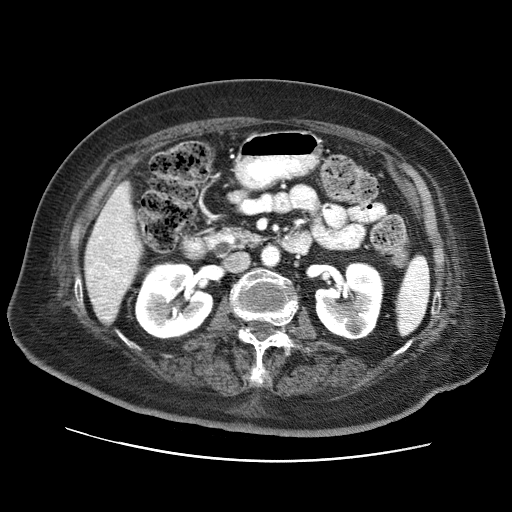
Contrast-enhanced abdominal CT (liver protocol), one axial slice; position 24 of 73 along the scan axis; 120 kVp; soft-tissue window (W 400 / L 40 HU); 2.5 mm slice thickness; 512 × 512 image matrix, field of view 380 × 380 mm. From the clinical record (not read from this slice): diagnosis: hepatocellular carcinoma (patient treated with transarterial chemoembolisation; whether this scan precedes or follows treatment is not stated here); TNM stage (as recorded): Stage-I; Child-Pugh class: A; tumour differentiation: well differentiated; tumour nodularity: uninodular.
Outlined on this slice (semi-automatically segmented with operator editing):
- liver parenchyma outside the tumour (the mass and vessels are separate outlines, so this box may not span the whole liver): bounding box [x1, y1, x2, y2] px = [84, 182, 140, 322]
- liver vessels: [89, 218, 134, 282]